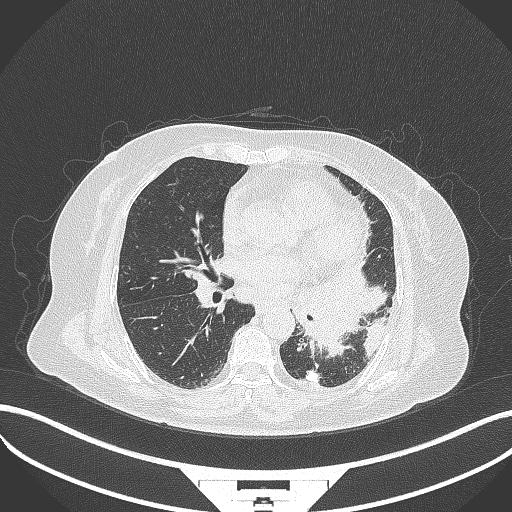
Chest CT, one axial slice; position 168 of 322 along the scan axis; lung window (W 1500 / L -600 HU); 1 mm slice thickness; 512 × 512 image matrix, field of view 400 × 400 mm. Patient: female, 69 years. From the clinical record (not read from this slice): clinical TNM (as recorded): T2b N3 M1.
Annotated regions visible in this slice (rectangle marked by the reading radiologist):
- lung tumour (recorded histology: adenocarcinoma): bounding box (x1, y1, x2, y2) in pixels: (298, 264, 388, 358)